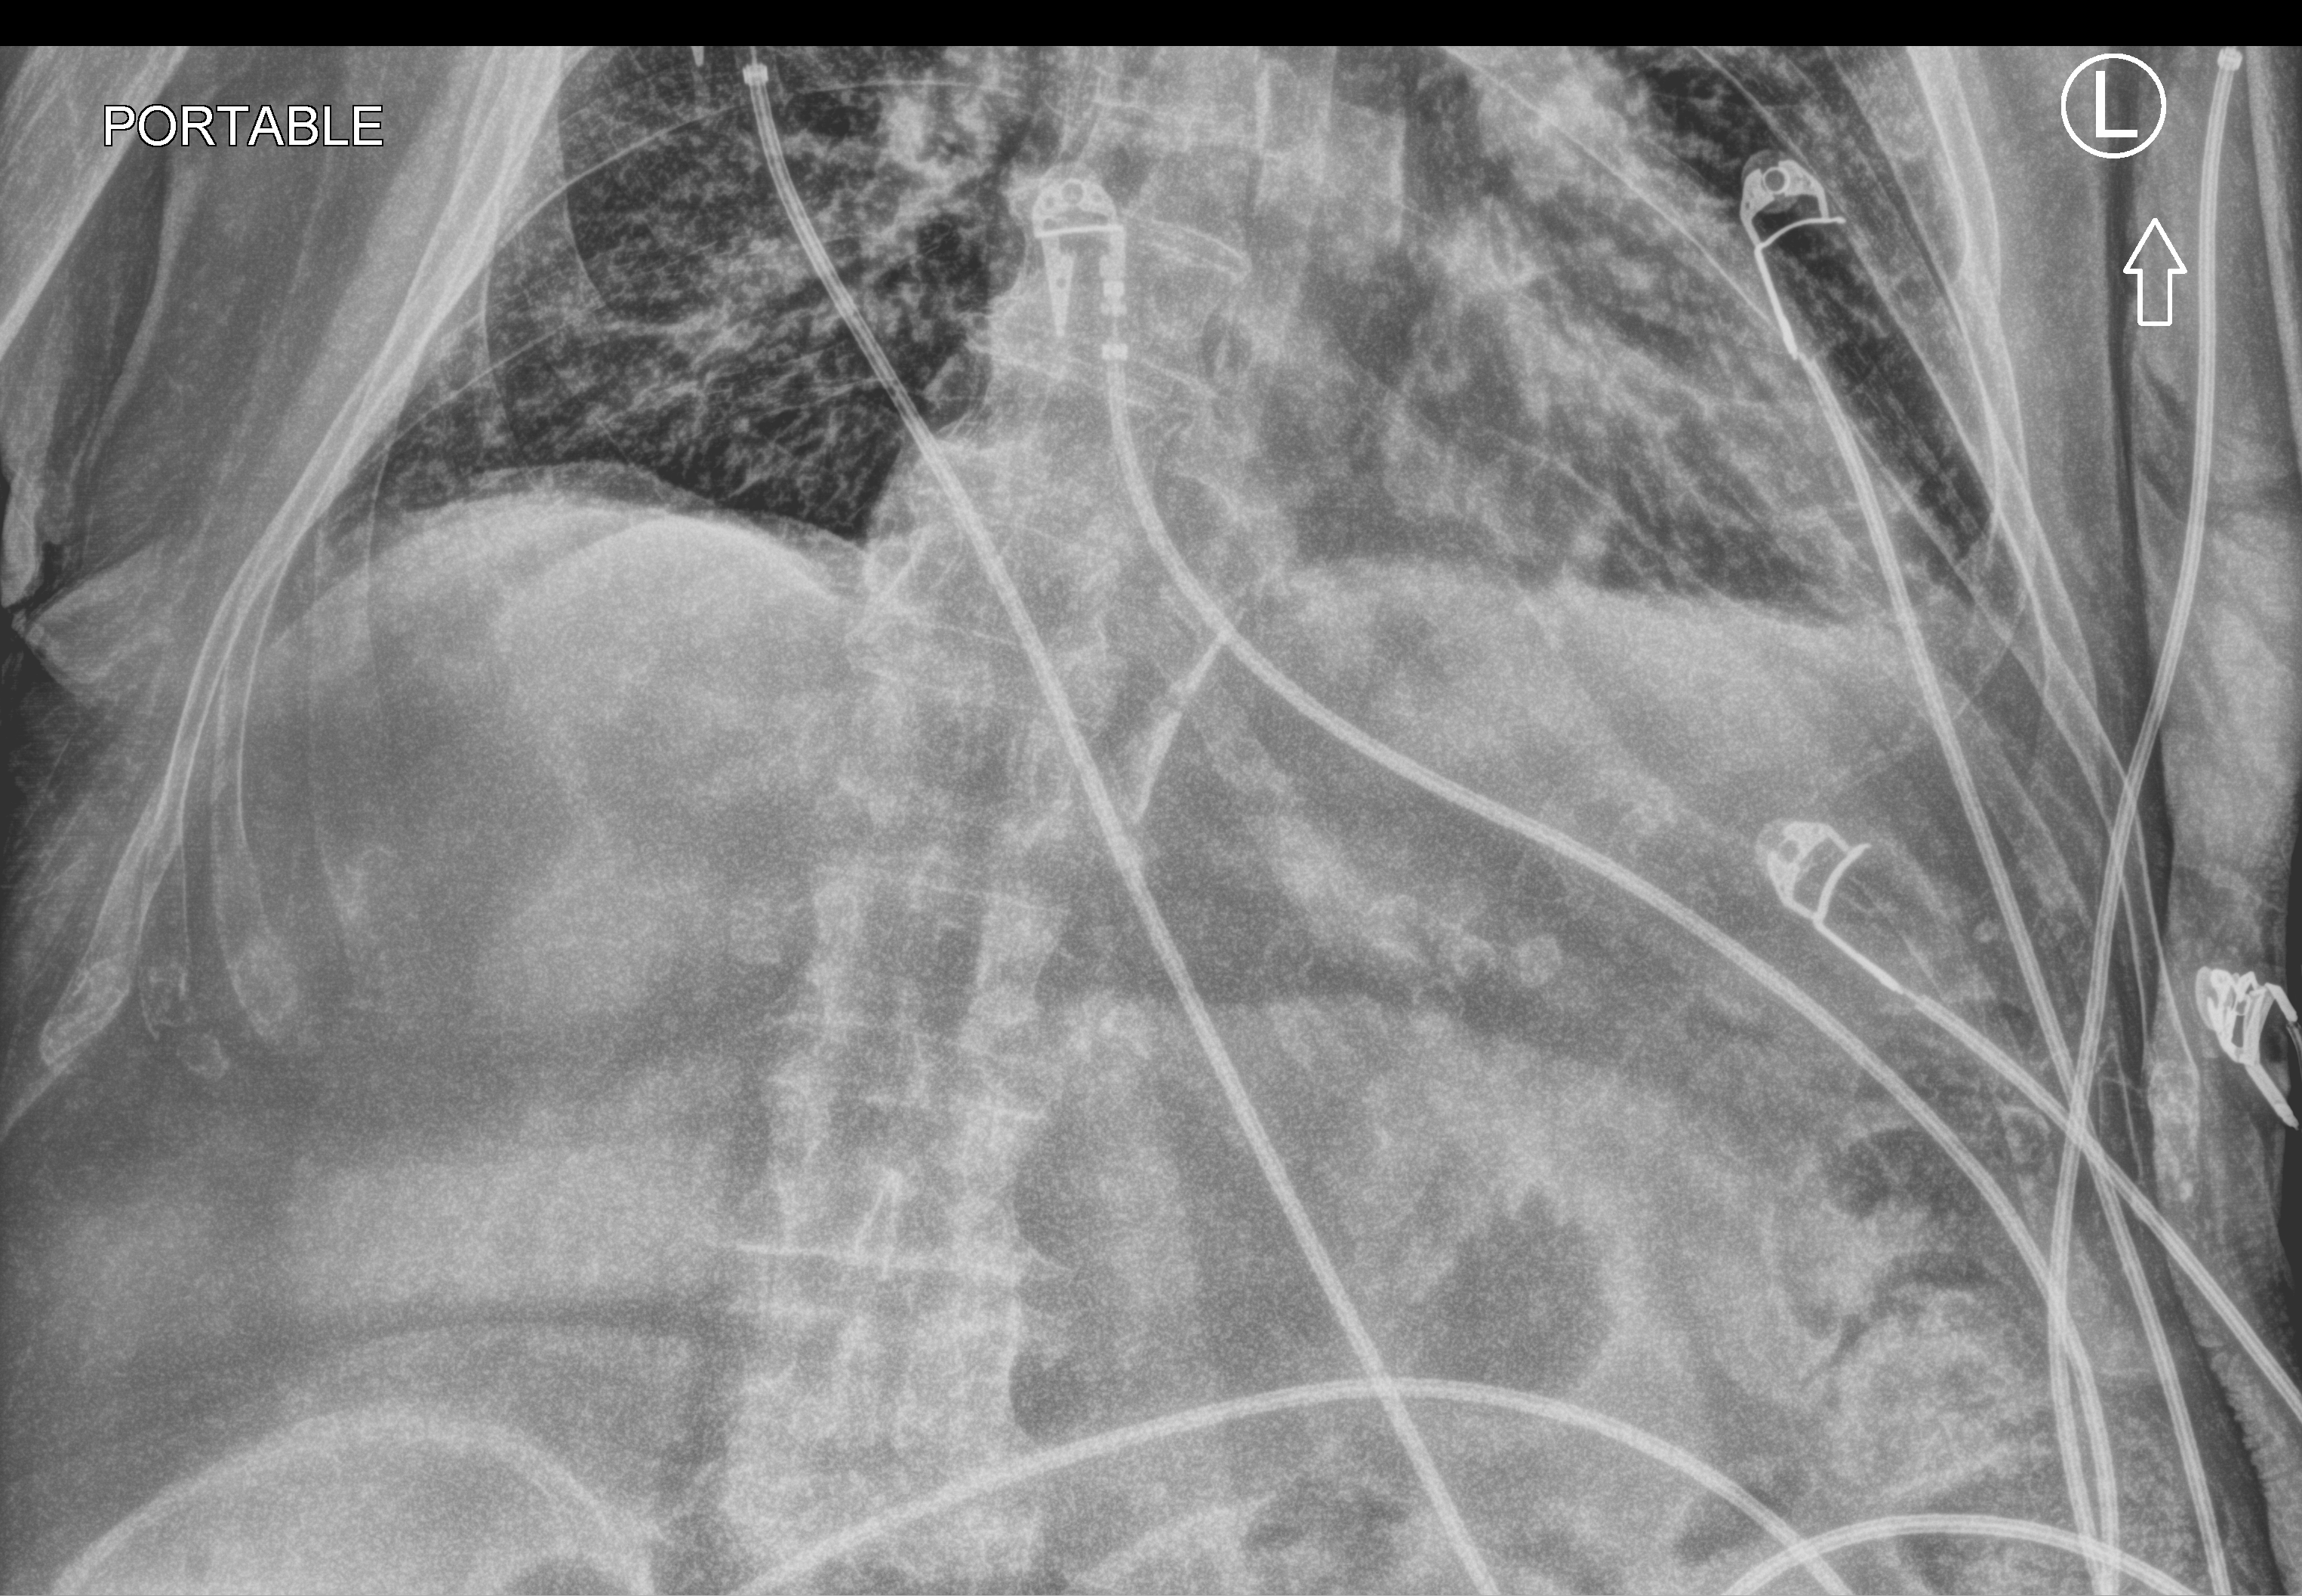
Portable abdomen radiograph, anteroposterior (AP) projection. Patient hospitalised with COVID-19; male, aged 75–90 years.
From the hospital-stay record, not from the radiograph (when in the stay this image was taken is not recorded):
- length of hospital stay: 10 days